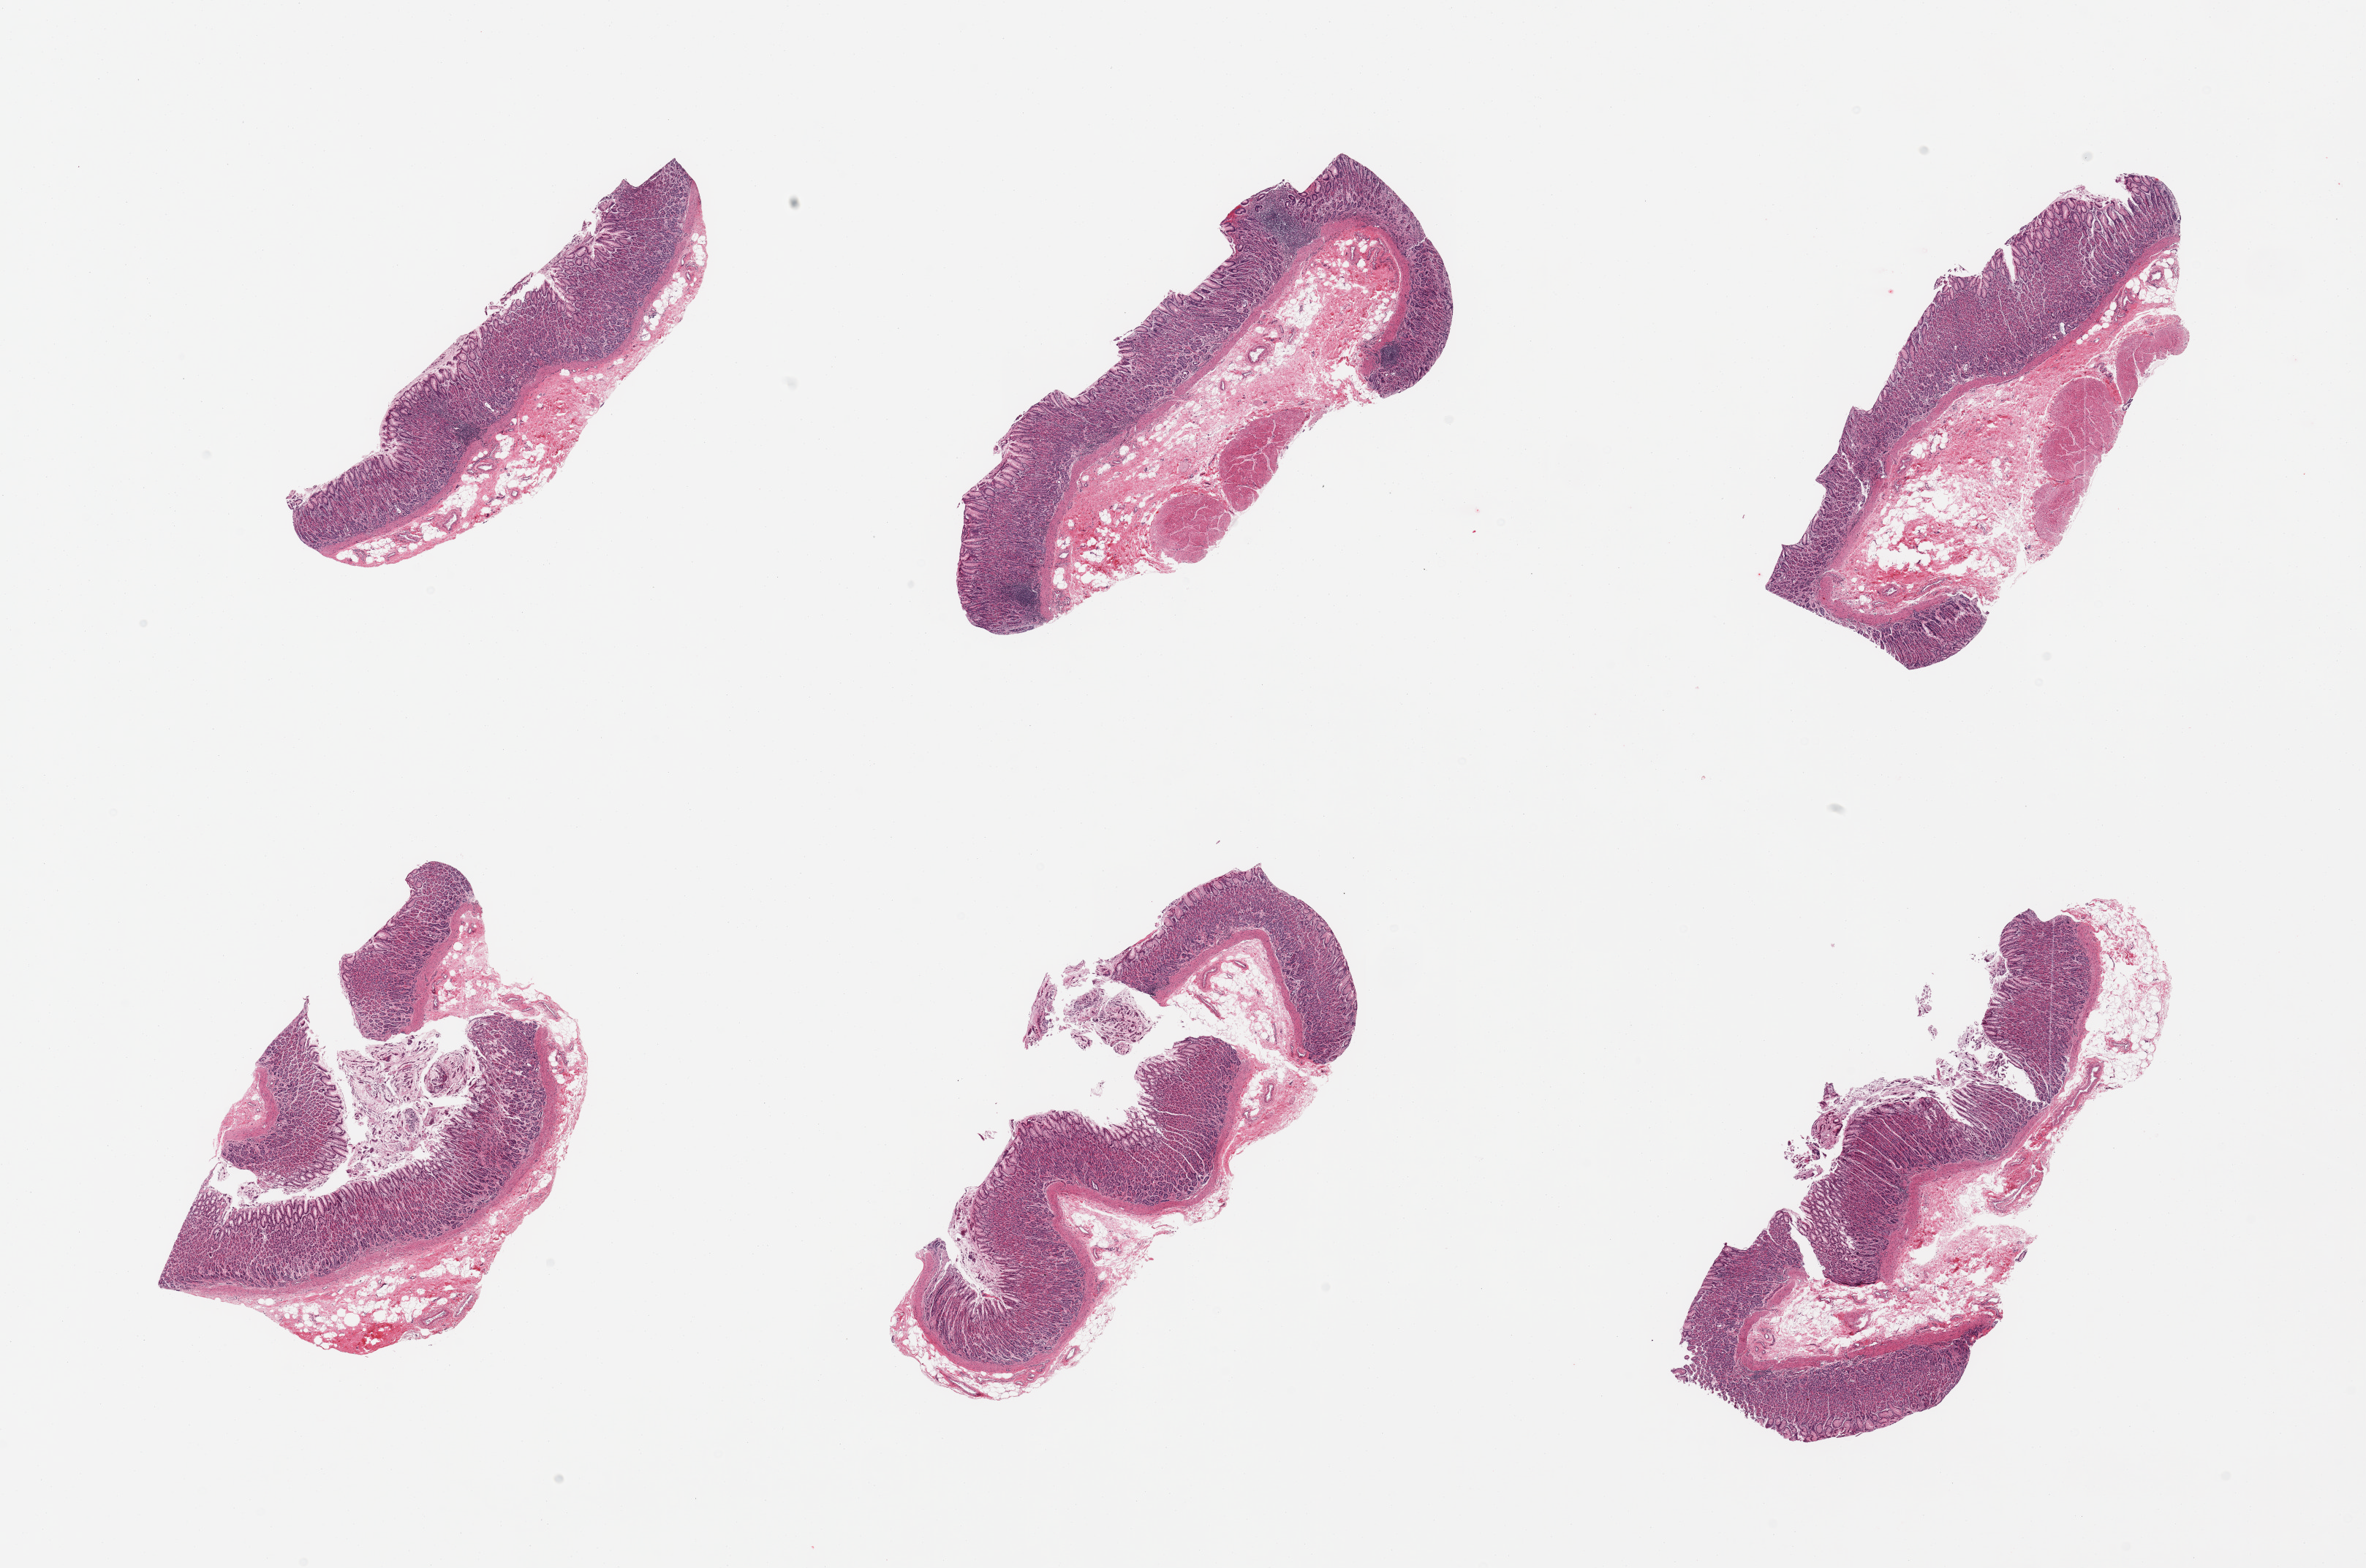
Digitized H&E-stained section — shown as a low-resolution overview of the whole scanned area (about 25.6 x 17.0 mm, acquisition: 20x scan), PAXgene-fixed, paraffin-embedded tissue, sampled site (target tissue): stomach, tissue donor sample. Donor: female.
Reviewer comment on this tissue sample: 6 pieces; well preserved gastric mucosa, lamina propria and muscularis (muscularis present in 2 of 6 pieces).